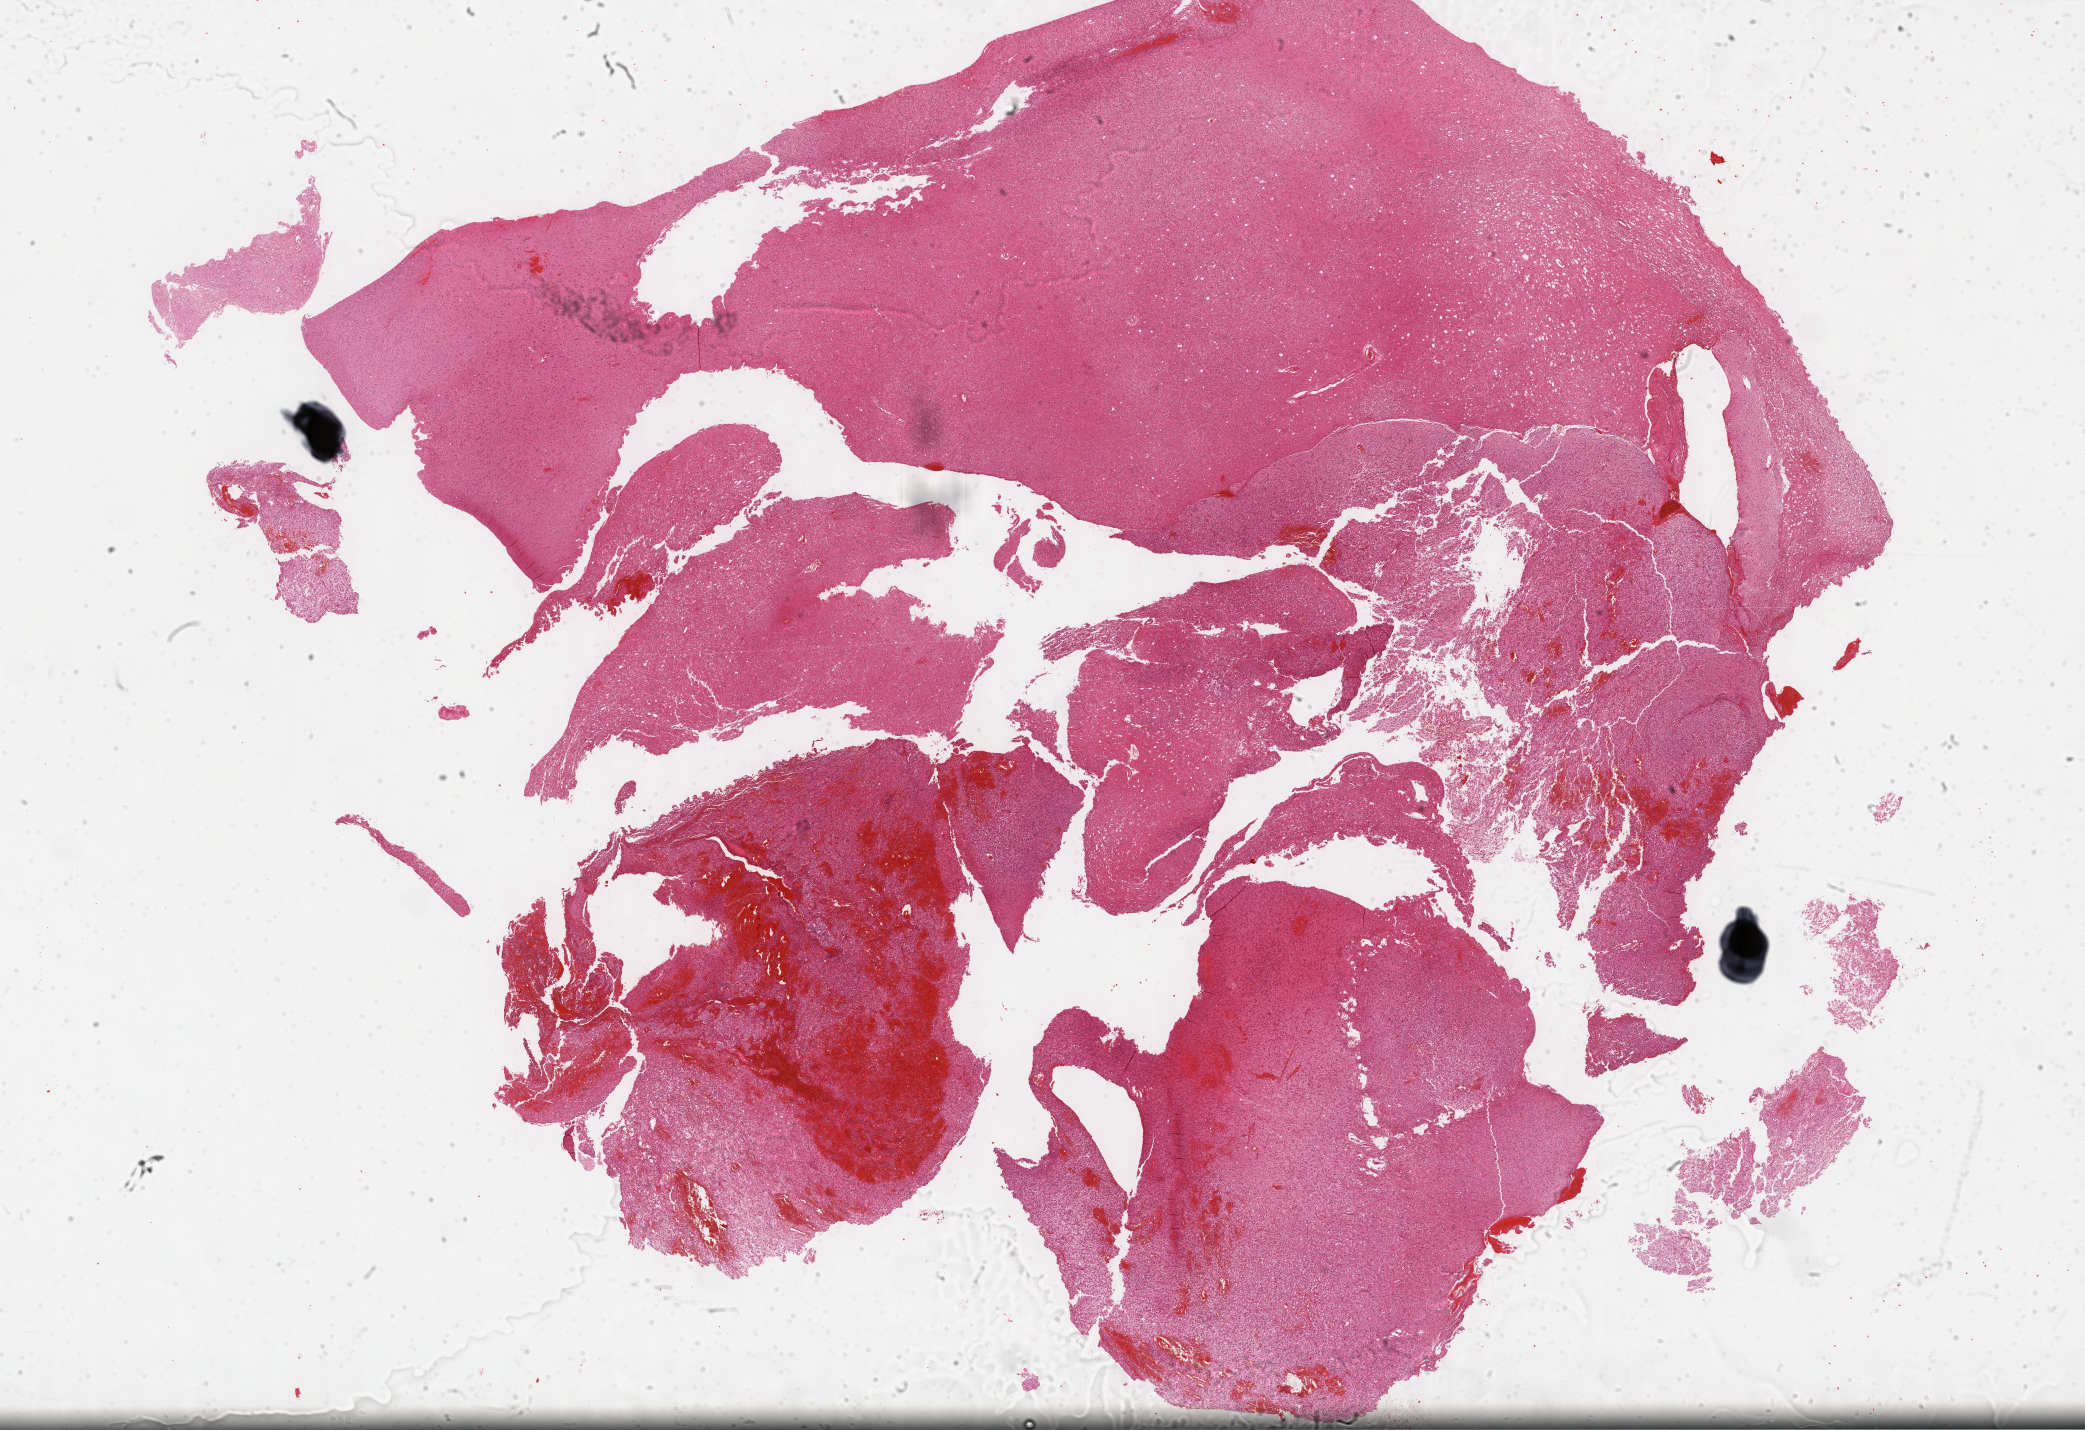
Digitized H&E-stained tissue section (whole slide), a low-resolution overview of the entire scanned area, about 33.7 x 23.1 mm. Formalin-fixed paraffin-embedded (FFPE) diagnostic section. Primary tumour sample from the brain. Patient: male, age at initial diagnosis 42 years. Histologic grade: G3 (poorly differentiated).
Histologic diagnosis: Mixed glioma (cerebrum).